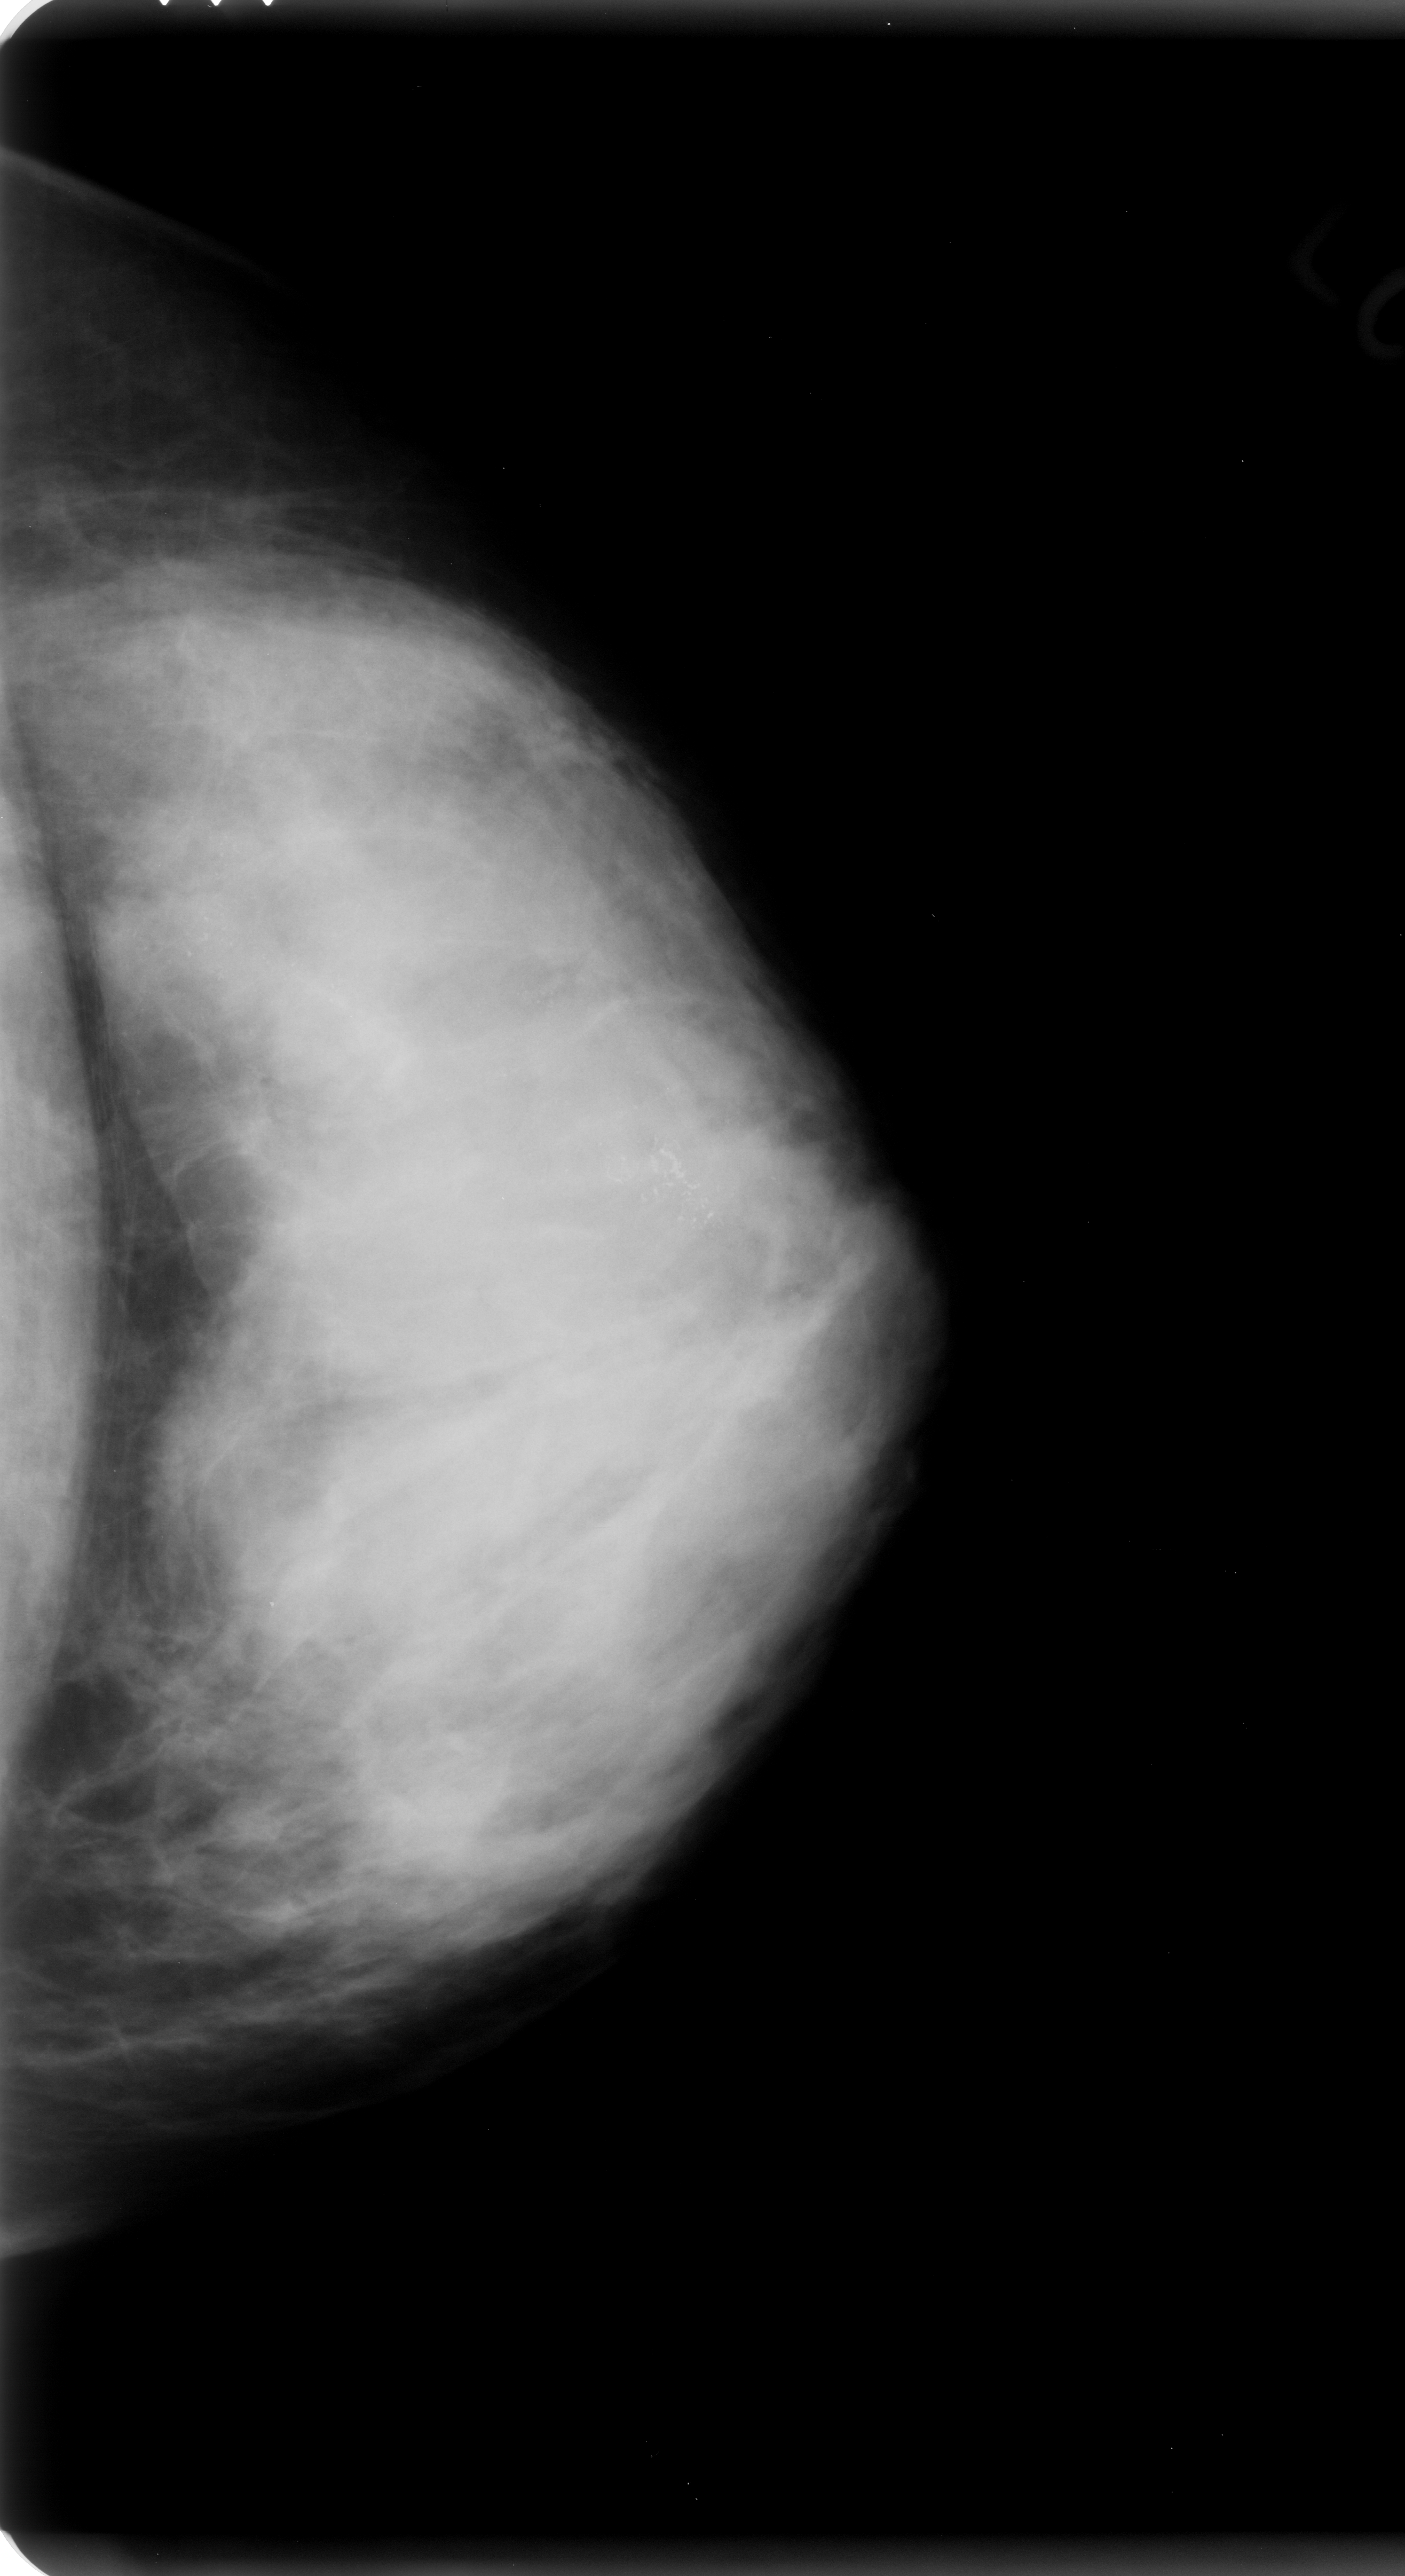
Digitized screen-film mammogram; left breast; CC view; BI-RADS breast density category 4 (scale 1–4).
Calcifications, morphology amorphous / pleomorphic, distribution segmental; BI-RADS assessment category 5; subtlety rating 5 on a 1 (subtle) to 5 (obvious) scale; pathology result (as recorded, not read from the image): malignant.